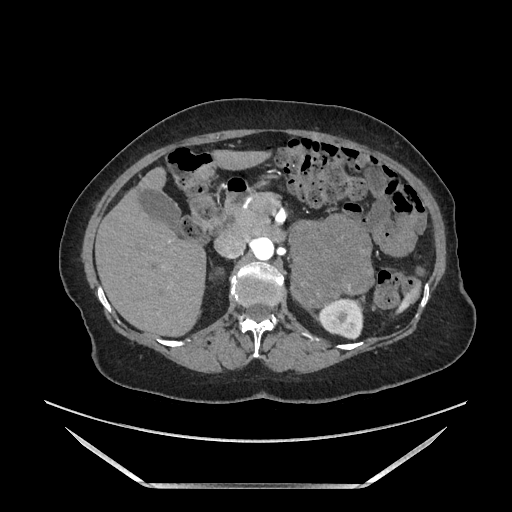
Contrast-enhanced abdominal CT, one axial slice; slice 101 of 205 in the series (ordered by position); soft-tissue window (W 400 / L 40 HU); 1.25 mm slice thickness; 512 × 512 image matrix, field of view 440 × 440 mm. Female patient. From the clinical record (not read from this slice): diagnosis: adrenocortical carcinoma; tumour side: left adrenal; tumour size at pathology: 12.5 cm; Ki-67 index: 39 %; stage (as recorded): 3.
Structures marked on this image (semi-automatically segmented with operator editing):
- mass: box from (x=292, y=216) to (x=372, y=305) px